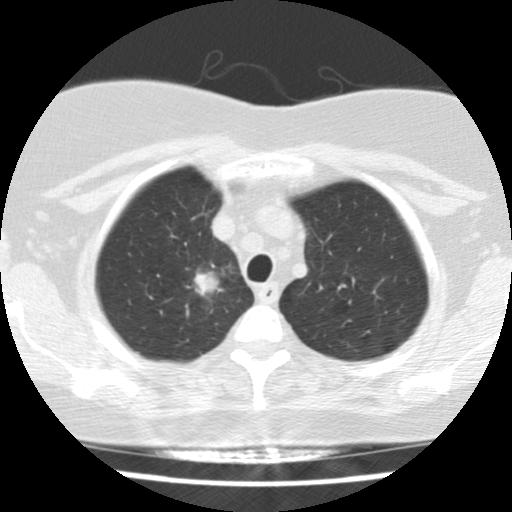
Low-dose screening chest CT, one axial slice. Position 125 of 148 along the scan axis. 120 kVp. Lung window (W 1500 / L -600 HU). 2.5 mm slice thickness. 512 × 512 image matrix, field of view 281 × 281 mm.
Annotated regions visible in this slice (manually delineated by an expert):
- lesion 1 (tumor, upper lobe of right lung): box from (x=194, y=272) to (x=220, y=296) px